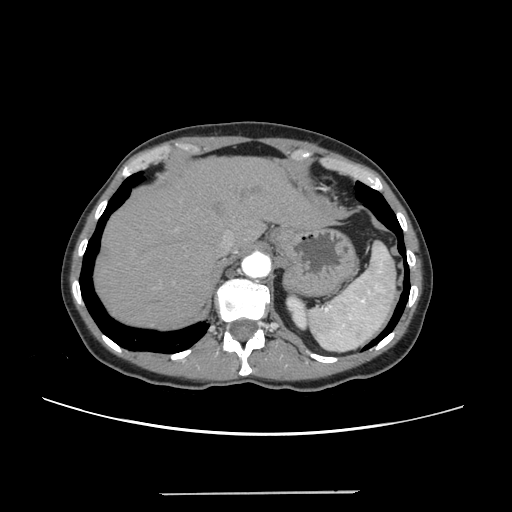
Contrast-enhanced abdominal CT, one axial slice; position 198 of 240 along the scan axis; intravenous contrast given; soft-tissue window (W 400 / L 40 HU); 512 × 512 image matrix, field of view 371 × 371 mm. Female patient, age 60 years. Case-level facts recorded for this patient, not image findings: diagnosis: colorectal cancer liver metastases, imaged before liver resection; multiple liver metastases: no; largest metastasis: 1.5 cm.
Annotated regions visible in this slice (outlined manually by an expert reader):
- hepatic veins: box from (x=219, y=219) to (x=248, y=251) px
- liver: (x=95, y=158)–(x=326, y=329)
- planned liver remnant (the part of the liver to remain after resection): (x=95, y=158)–(x=325, y=329)